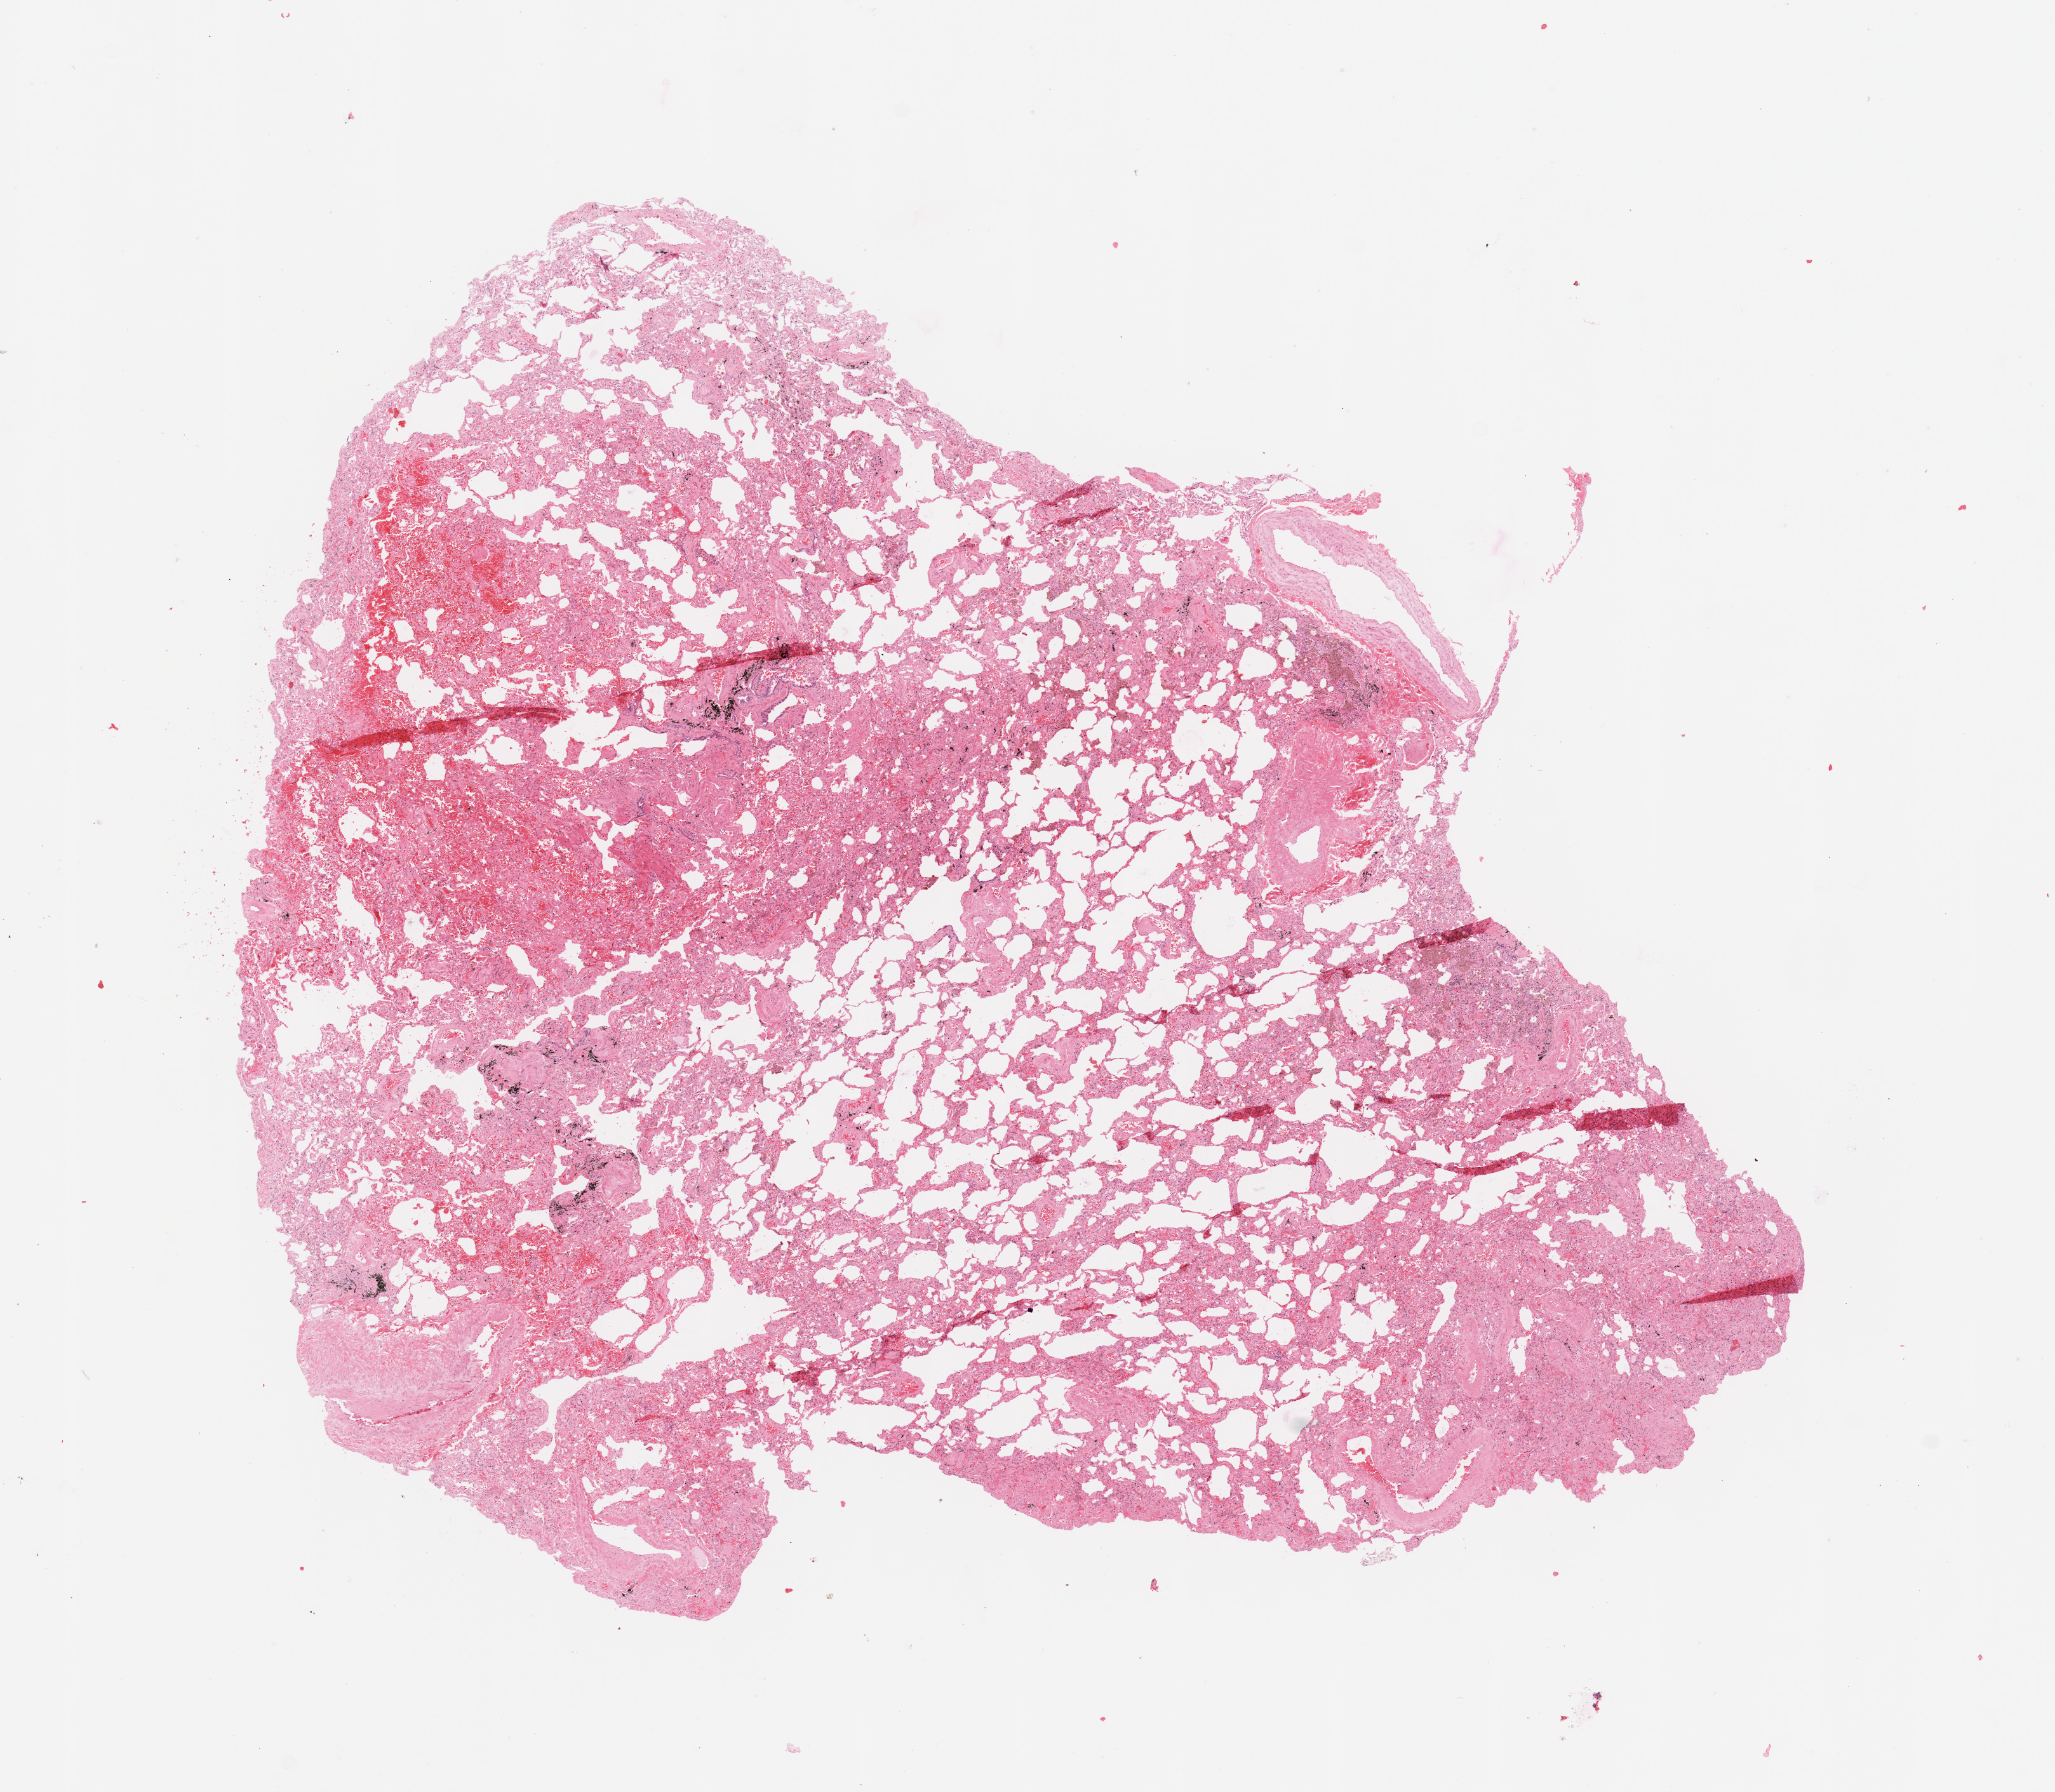
Whole-slide histology image, Hematoxylin and eosin (H&E) stained, a low-resolution overview of the entire scanned area, about 12.8 x 11.2 mm. Normal (non-tumour) tissue sample, sampled site: lung. Male, 68 y/o.
This section: normal (non-tumour) tissue from the same patient. Patient diagnosis: Adenocarcinoma, NOS.